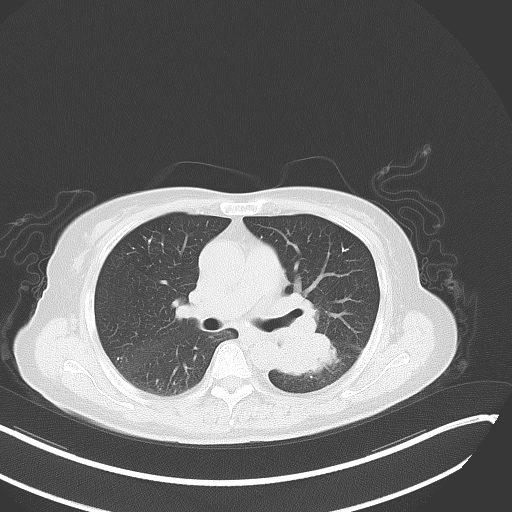
Chest CT, one axial slice. Position 23 of 48 along the scan axis. 120 kVp. Lung window (W 1500 / L -600 HU). 5 mm slice thickness. 512 × 512 image matrix, field of view 400 × 400 mm. Female patient, age 64 years. Case-level facts recorded for this patient, not image findings: clinical TNM (as recorded): T3 N1 M1; histopathological grade: G3.
Structures marked on this image (bounding box drawn by a radiologist):
- lung tumour (recorded histology: small cell carcinoma): bounding box (x1, y1, x2, y2) in pixels: (267, 322, 337, 375)